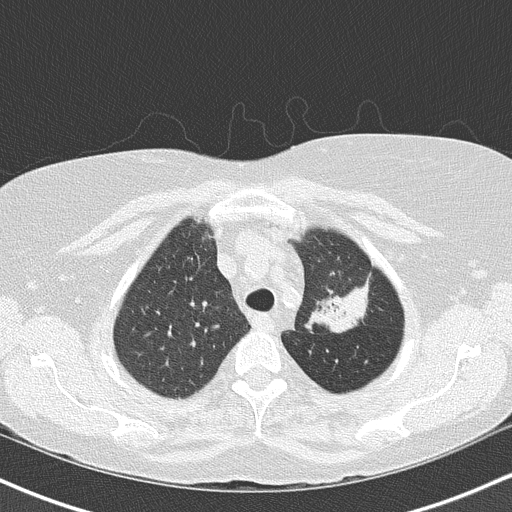
Axial slice from a low-dose chest CT screening exam; third annual screen; lung window (W 1500 / L -600 HU); lung (sharp) reconstruction kernel (B50f); slice 122 of 147 in the series; 512 × 512 image matrix. Female participant, aged 68 years at enrolment.
Expert-annotated lung lesion, bounding box <291,230,380,337> (left, top, right, bottom; pixels). The exam's reader record, not a measurement of the box and not confirmed to be the same lesion: non-calcified nodule or mass ≥4 mm, left upper lobe, 5 × 5 mm, poorly defined margins, mixed attenuation, pre-existing on the prior screen: yes; interval growth: yes. Later outcome: lung cancer diagnosed 42 days after this screen — adenocarcinoma, NOS, left upper lobe, poorly differentiated (G3), stage IB (AJCC 6th edition), 50 mm at pathology.